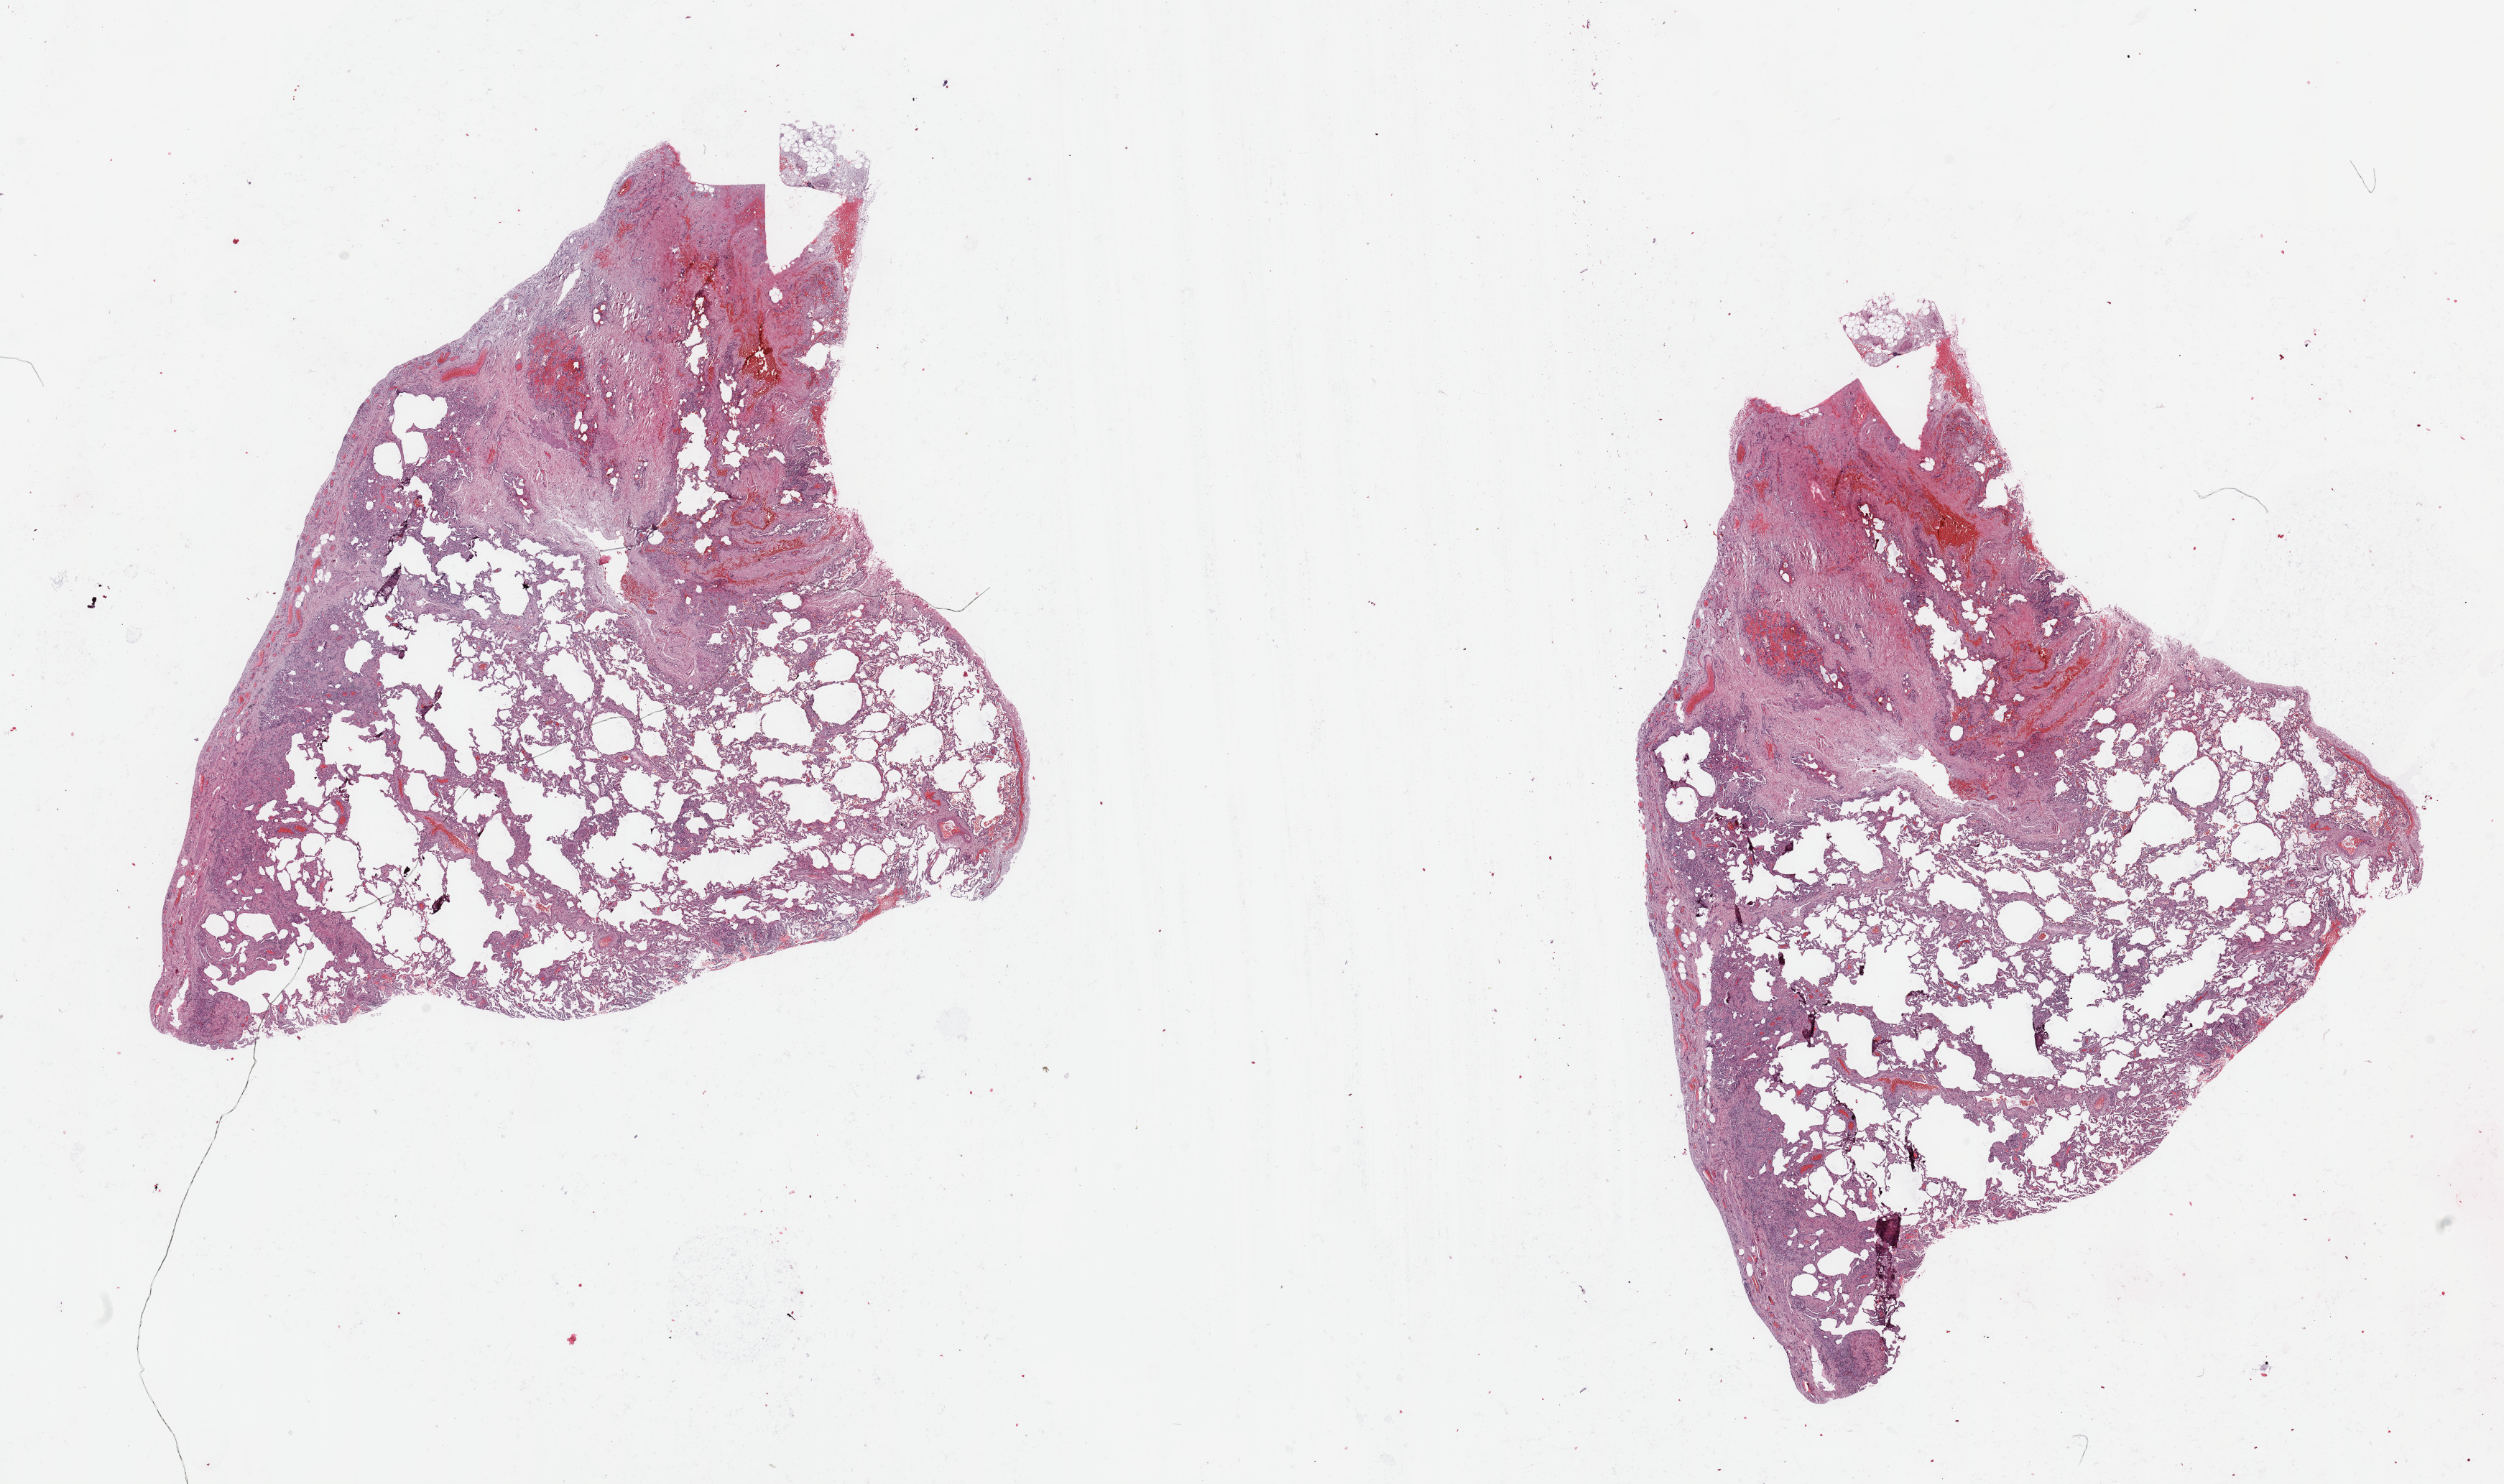
Digitized H&E-stained tissue section (whole slide) — shown as a low-resolution overview of the whole scanned area (about 27.6 x 16.3 mm, slide scanned at 20x), normal (non-tumour) tissue sample, sampled site: lung. 54-year-old male patient.
This section: normal (non-tumour) tissue from the same patient. Patient diagnosis: Squamous cell carcinoma, NOS.